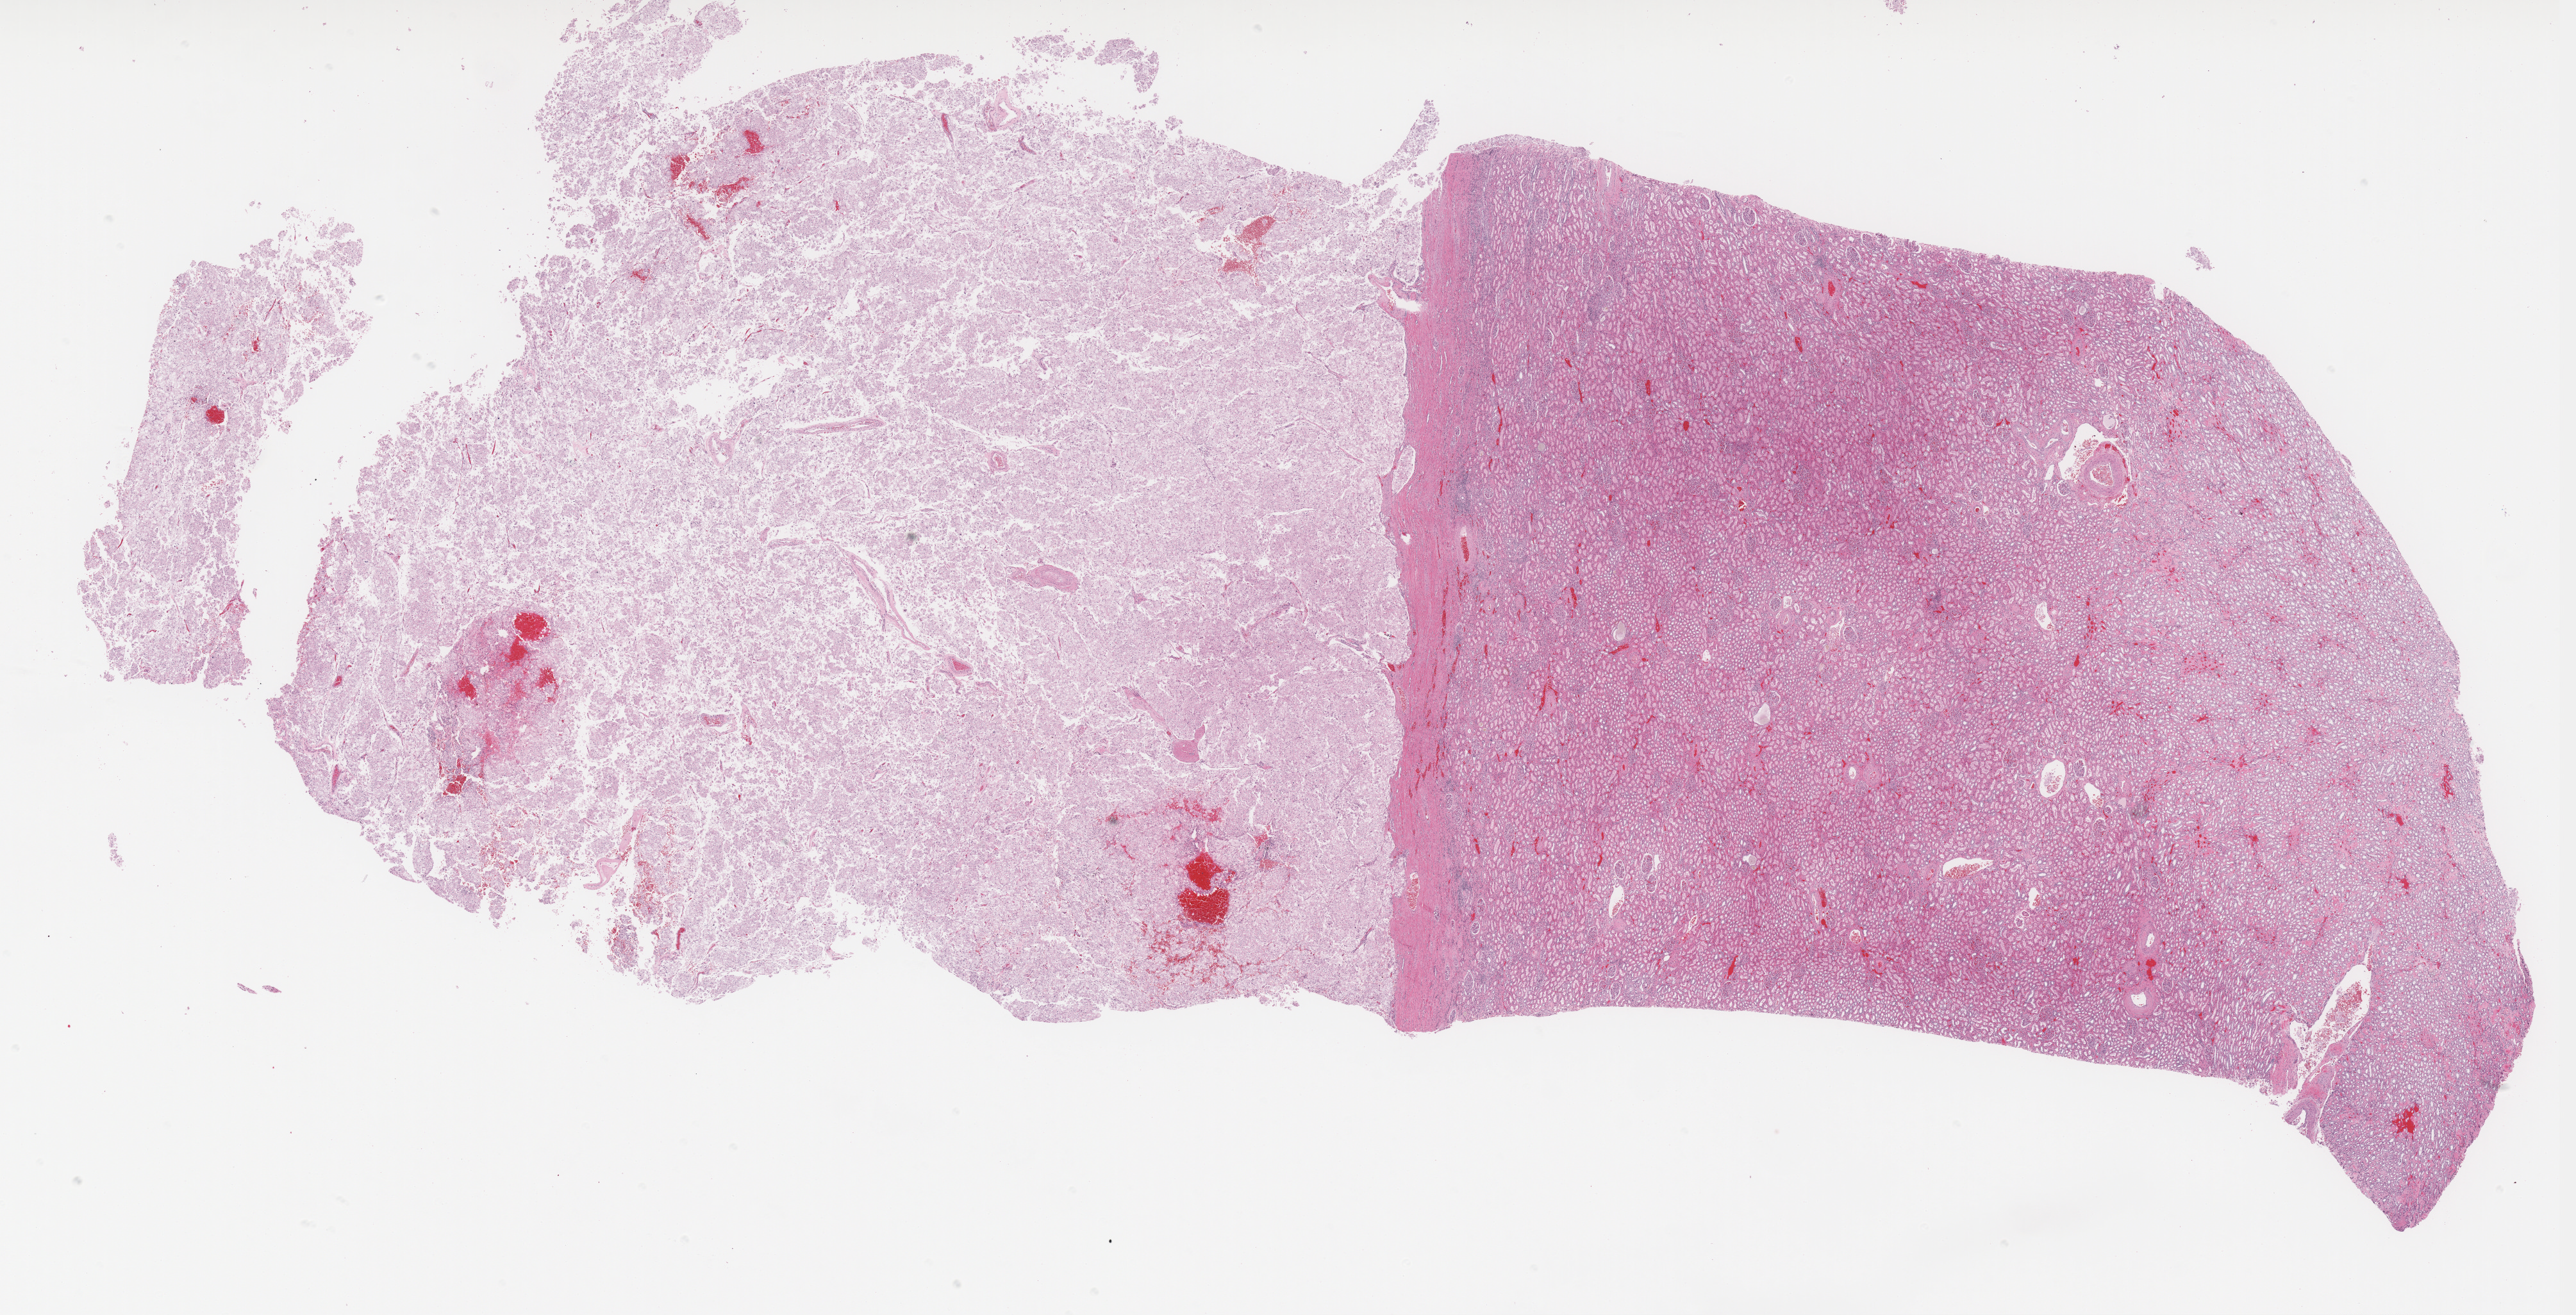
H&E whole-slide image — low-resolution overview of the scanned area, about 32.1 x 16.4 mm. Formalin-fixed paraffin-embedded (FFPE) diagnostic section. Kidney, primary tumour sample. Male, age 51 years at initial diagnosis.
• histologic diagnosis: Renal cell carcinoma, chromophobe type
• laterality: left
• AJCC pathologic stage: III